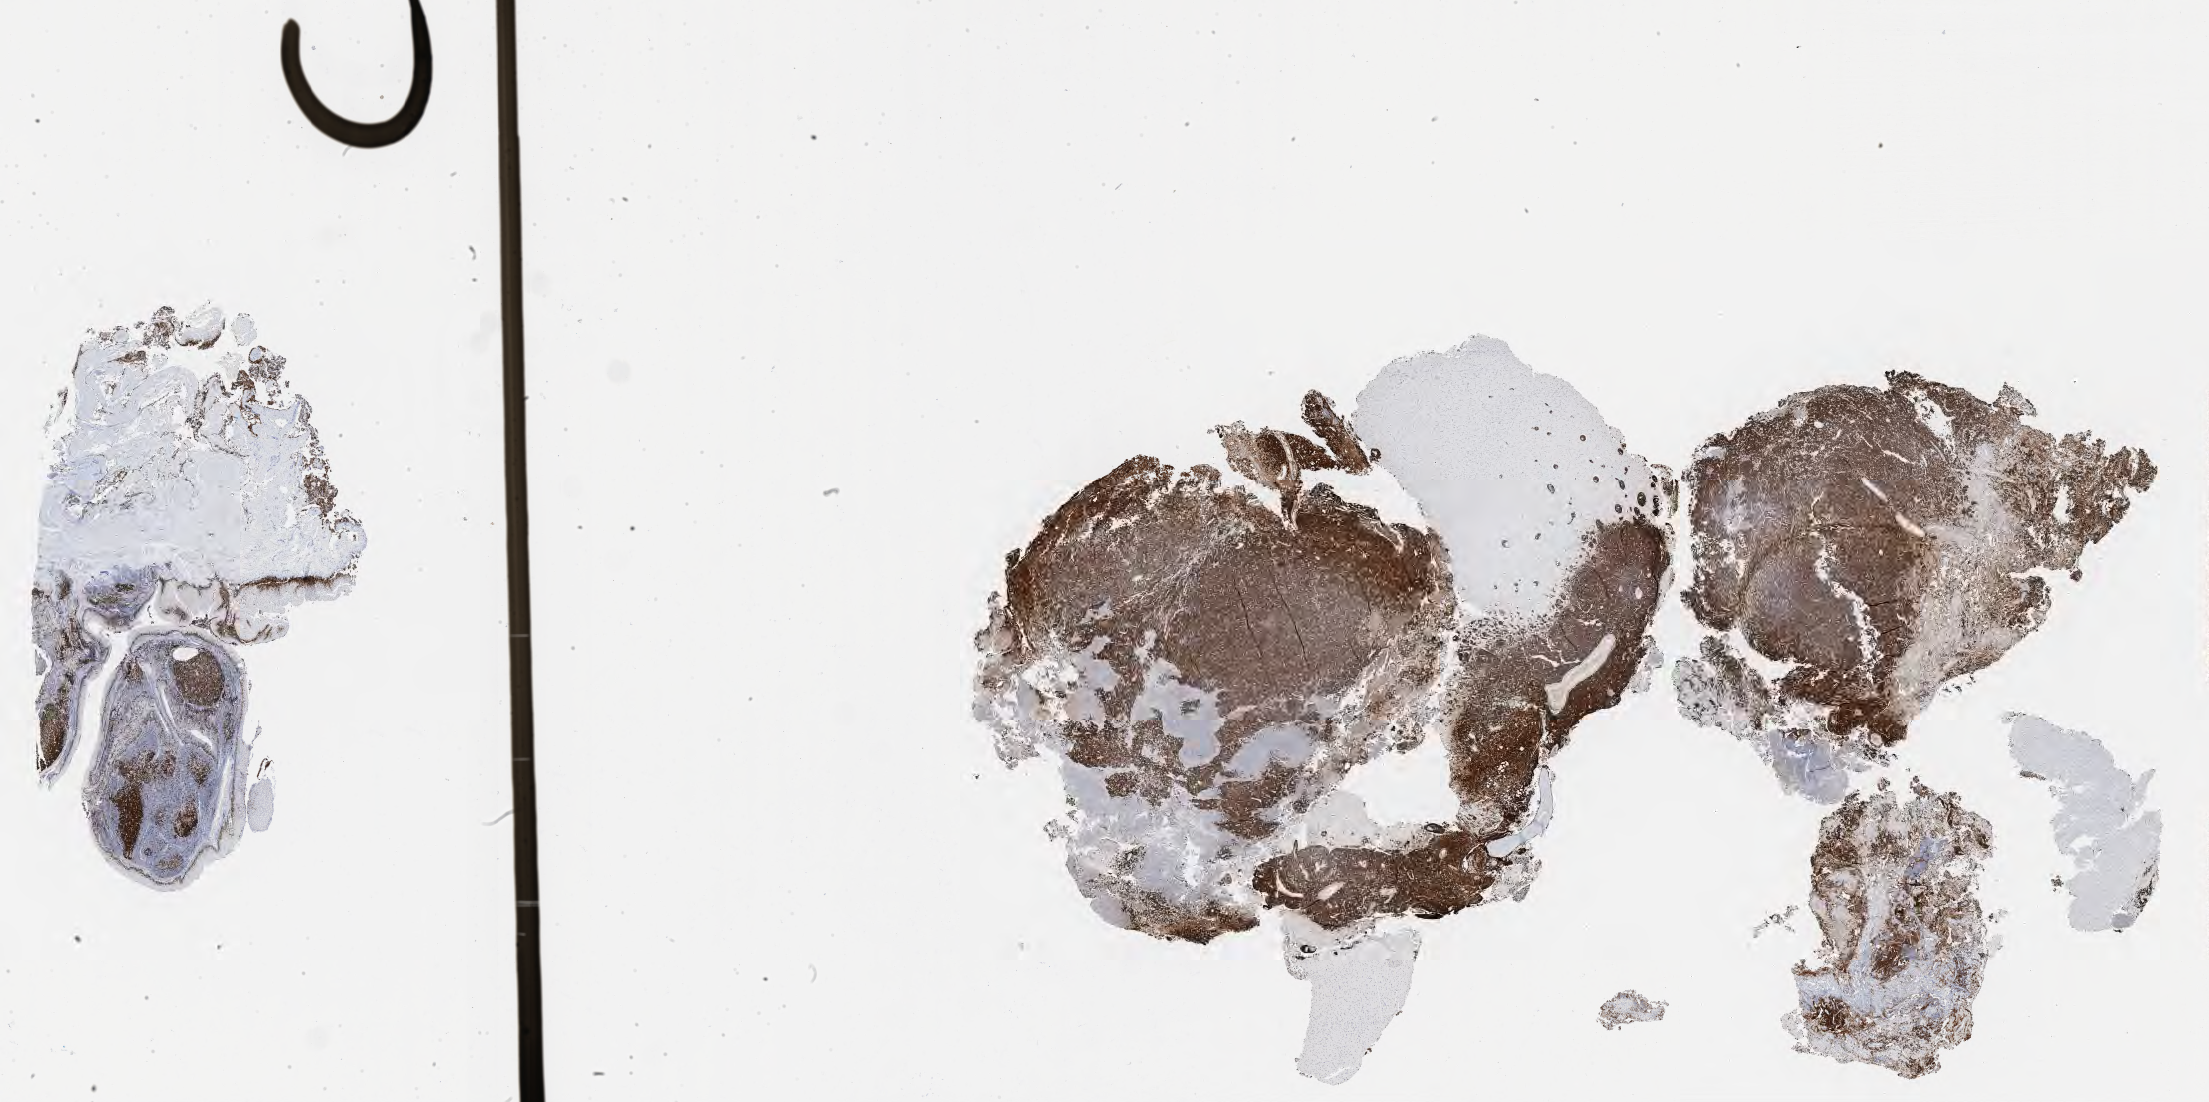
Immunohistochemistry (IHC) whole-slide image stained for Ki-67, whole scanned area (about 35.7 x 17.8 mm) shown as a low-resolution overview, tumor tissue. Patient female; age 73 years.
Histologic diagnosis: Burkitt lymphoma, NOS.